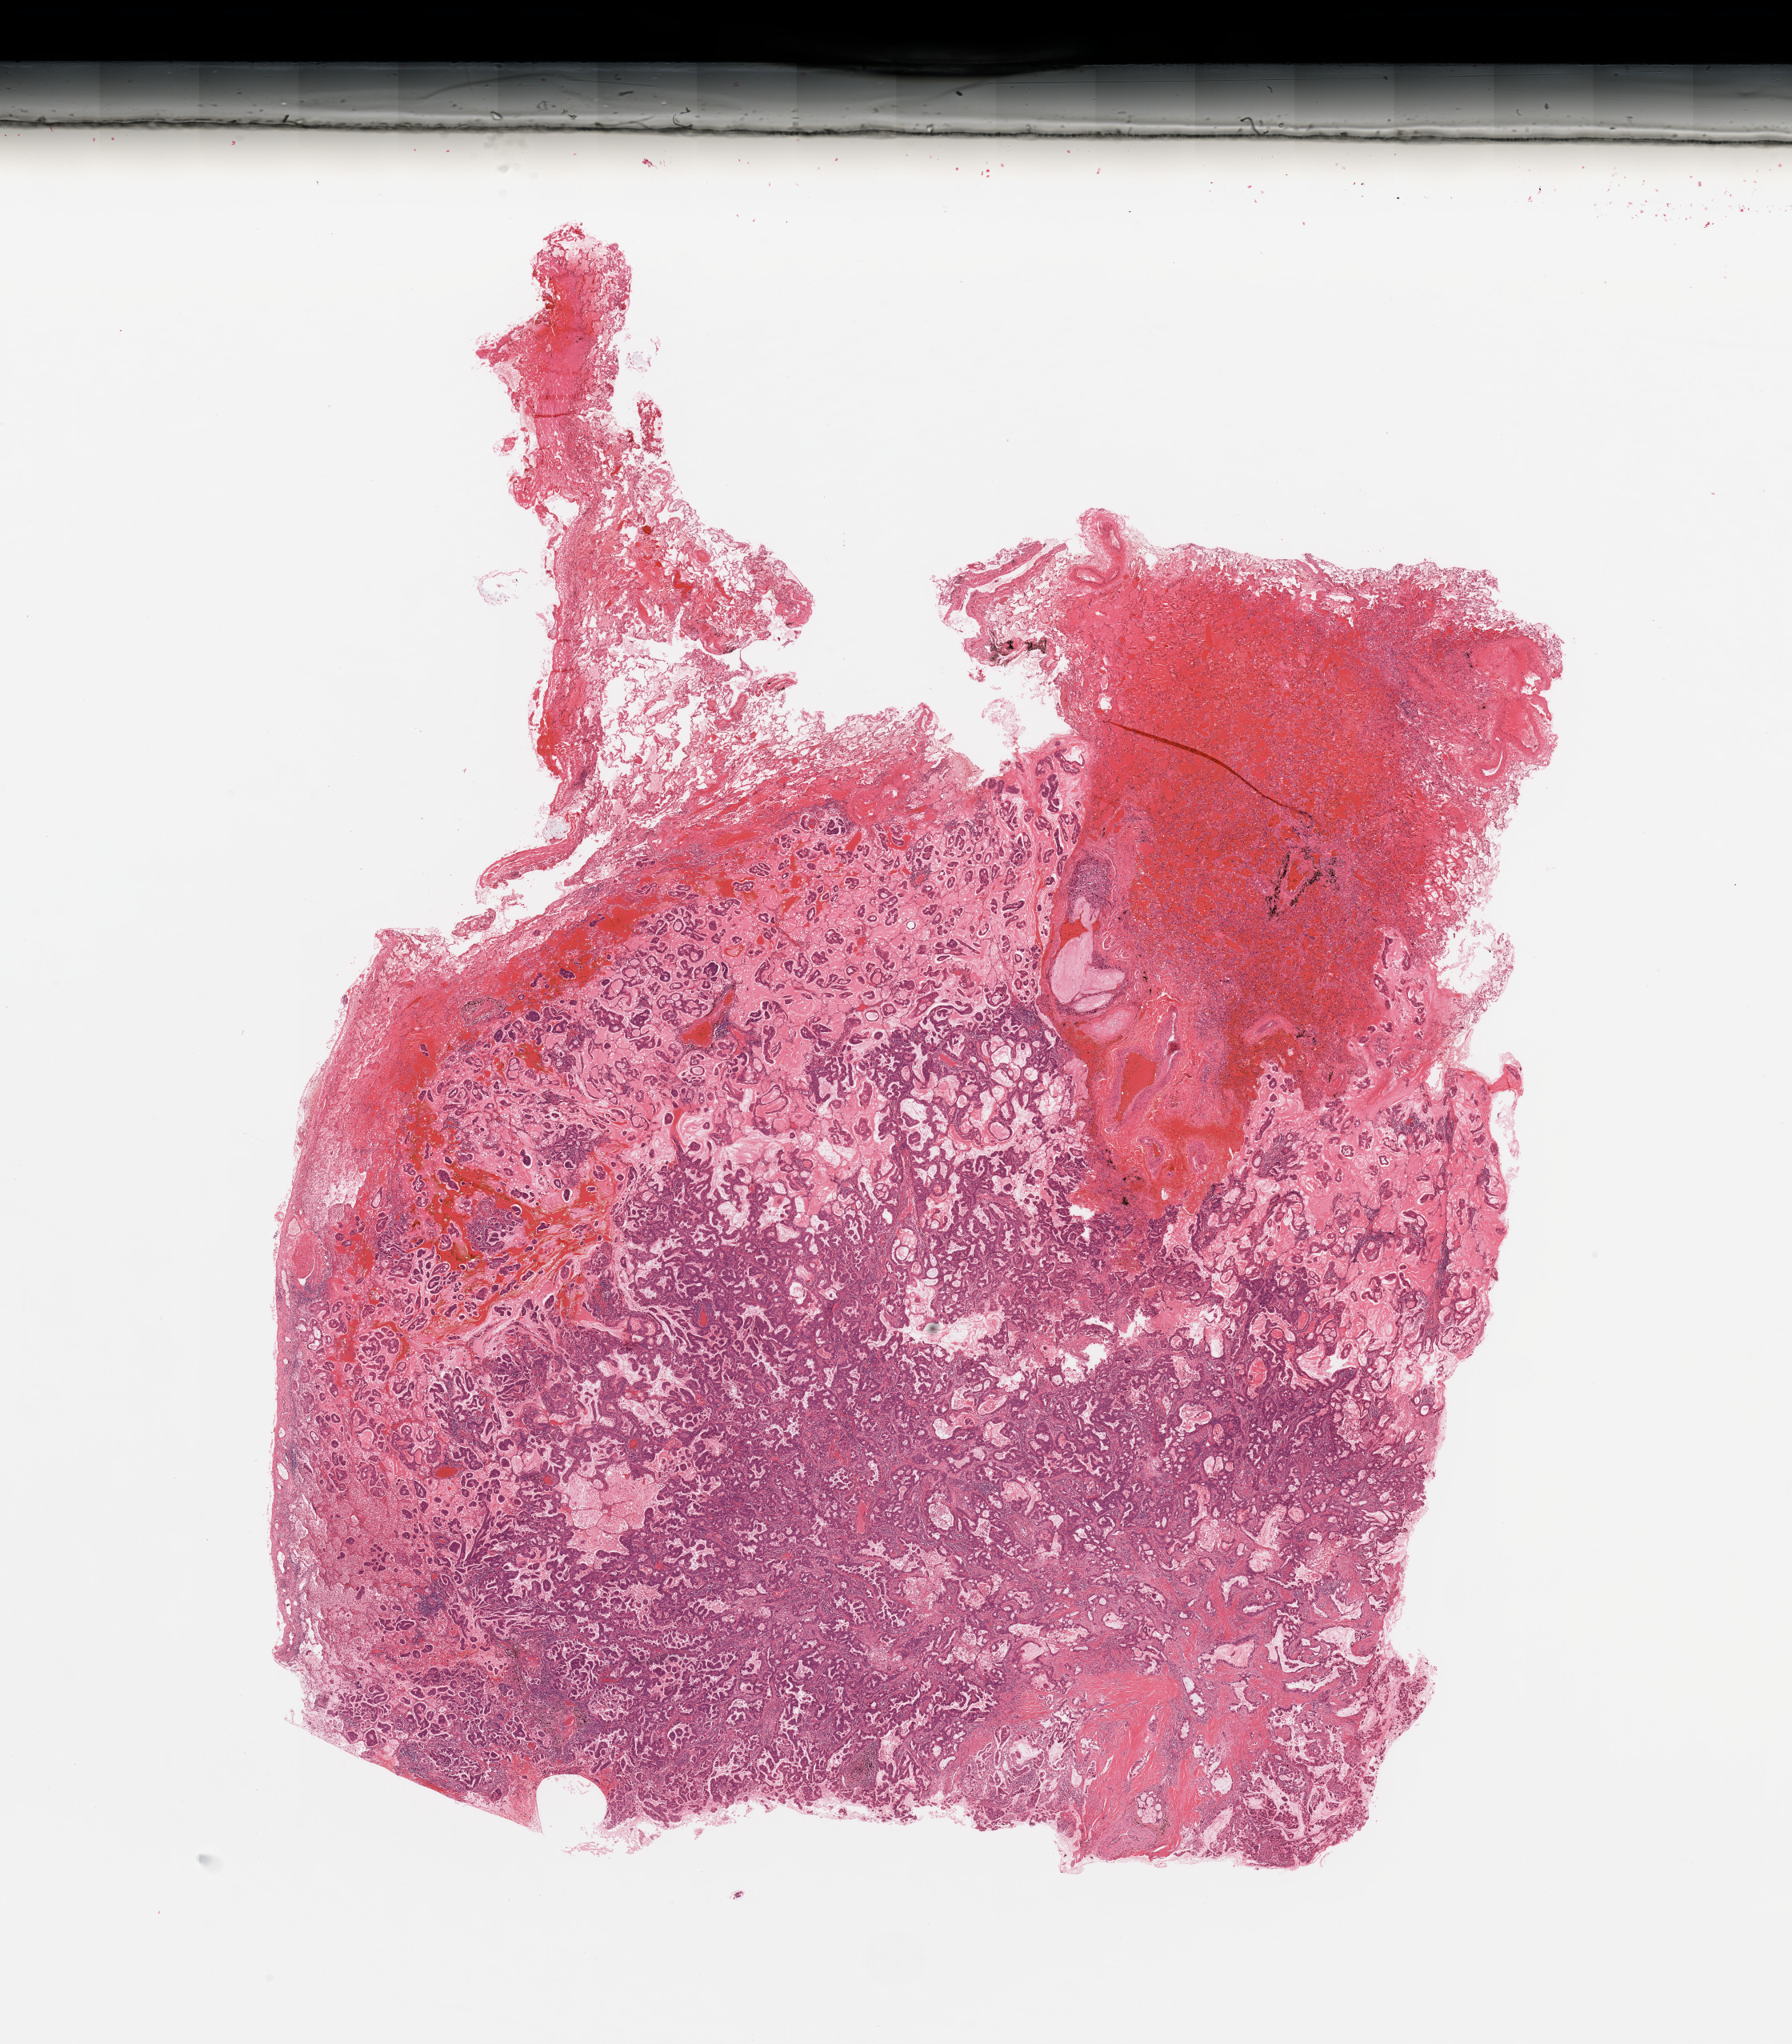
Whole-slide histology image, H&E-stained, whole scanned area (about 17.7 x 20.2 mm, from a 20x scan) shown as a low-resolution overview, lung, tumour tissue. Female, 52 y/o. Histologic grade: G2 (moderately differentiated).
• AJCC pathologic stage: IIA
• histologic diagnosis: Adenocarcinoma, NOS
• primary tumour site (as recorded): left lower lobe